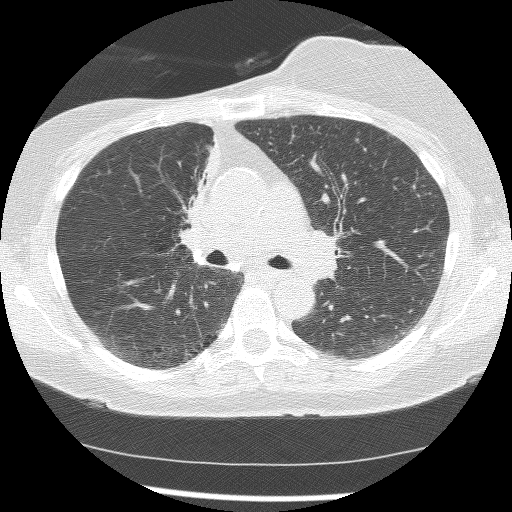
Chest CT (low-dose screening protocol), one axial image; baseline annual screen; lung window (W 1500 / L -600 HU); 2.5 mm slice thickness; lung (sharp) reconstruction kernel (BONE); 120 kVp. Female, age 56 years at enrolment.
• Expert-annotated lung lesion, bounding box <161,146,216,258> (left, top, right, bottom; pixels).
• The screening reader recorded 2 non-calcified nodules or masses ≥4 mm on this exam (right lower lobe, right middle lobe); which of them this box marks is not recorded.
• Official screen result: positive, change unspecified: nodule(s) >= 4 mm or enlarging nodule(s), mass(es), or other non-specific abnormalities suspicious for lung cancer.
• Later outcome: lung cancer diagnosed 1185 days after this screen (after the third annual screen) — adenocarcinoma, NOS, right upper lobe, stage IIIB (AJCC 6th edition), 8 mm at pathology.